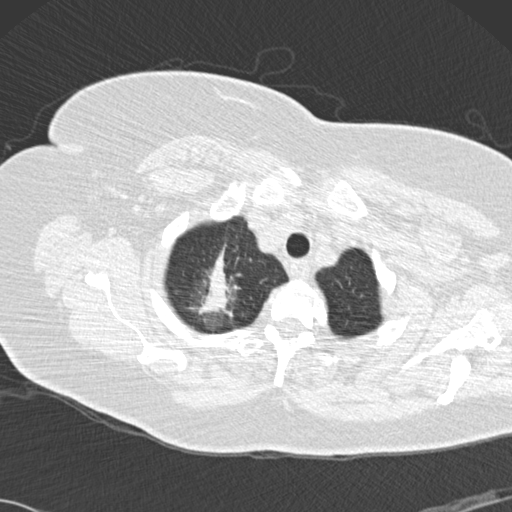
Low-dose screening chest CT, one axial slice; slice 129 of 146 in the series (ordered by position); reconstruction kernel B30f; 120 kVp; lung window (W 1500 / L -600 HU); 512 × 512 image matrix, field of view 350 × 350 mm.
Annotated regions visible in this slice (outlined manually by an expert reader):
- lesion 1 (tumor, upper lobe of right lung): bounding box (x1, y1, x2, y2) in pixels: (191, 249, 239, 317)